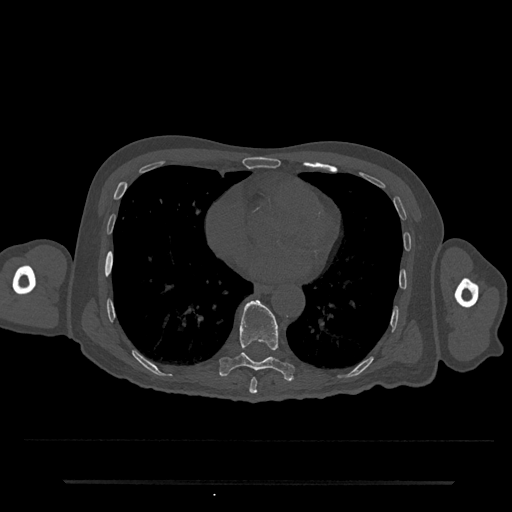
CT including the spine, one axial slice; position 371 of 797 along the scan axis; reconstruction kernel Br40s/3; 120 kVp; bone window (W 1800 / L 400 HU); 0.5 mm slice thickness; 512 × 512 image matrix, field of view 427 × 427 mm. Patient: male, 74 years. Case-level facts recorded for this patient, not image findings: primary cancer: prostate.
Structures marked on this image (semi-automatically segmented with operator editing):
- T8 vertebra: bounding box (x1, y1, x2, y2) in pixels: (249, 378, 257, 394)
- T9 vertebra: (219, 300, 295, 380)